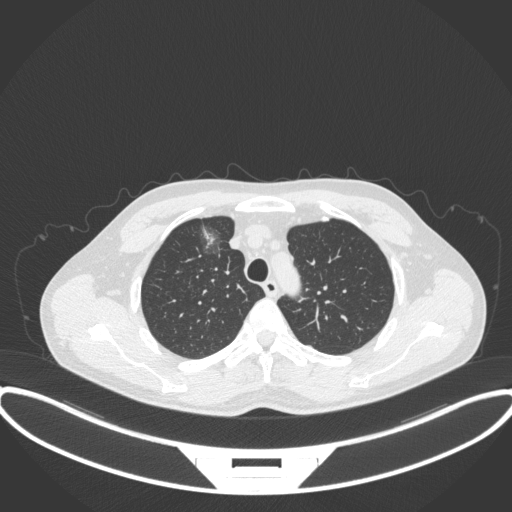
Chest CT, one axial slice; position 289 of 395 along the scan axis; reconstruction kernel B31f; 120 kVp; lung window (W 1500 / L -600 HU); 1 mm slice thickness; 512 × 512 image matrix. Patient: male, 60 years. Case-level facts recorded for this patient, not image findings: clinical TNM (as recorded): T1c N0 M0.
Structures marked on this image (rectangle marked by the reading radiologist):
- lung tumour (recorded histology: adenocarcinoma): bounding box [x1, y1, x2, y2] px = [197, 218, 226, 263]